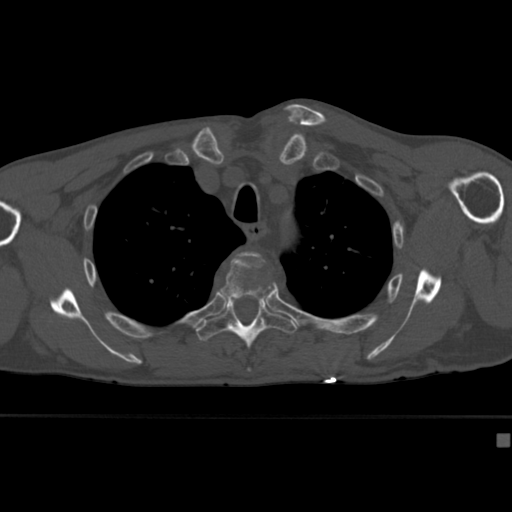
CT including the spine, one axial slice. Position 315 of 430 along the scan axis. Reconstruction kernel Br40s. 120 kVp. Bone window (W 1800 / L 400 HU). 1.5 mm slice thickness. 512 × 512 image matrix, field of view 337 × 337 mm. Male patient, age 64 years. Case-level facts recorded for this patient, not image findings: primary cancer: uterus; vertebrae with lytic lesions (as recorded): T1, T4, T5, T7, L5.
Outlined on this slice (semi-automatic segmentation, software-assisted and operator-edited):
- T3 vertebra: box from (x=240, y=251) to (x=259, y=255) px
- T4 vertebra: (x=220, y=253)–(x=277, y=371)
- T5 vertebra: (x=196, y=296)–(x=298, y=349)